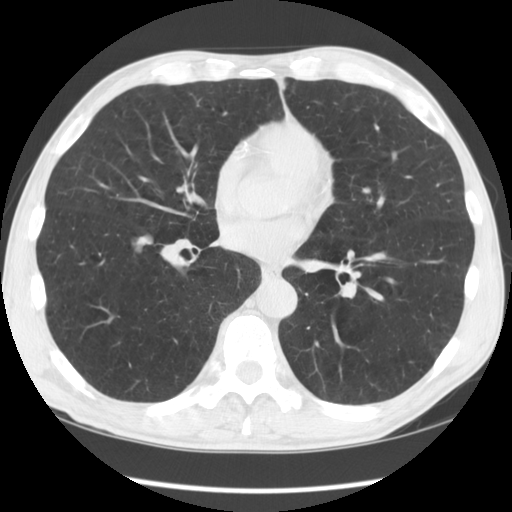
Chest CT (low-dose screening protocol), one axial image; second annual screen; lung window (W 1500 / L -600 HU); 2.5 mm slice thickness; standard (soft-tissue) reconstruction kernel (STANDARD); slice 83 of 135 in the series. Male, age 60 years at enrolment.
Expert reader's lesion annotation, bounding box <111,229,164,269> (left, top, right, bottom; pixels). The exam's reader record, not a measurement of the box and not confirmed to be the same lesion: non-calcified nodule or mass ≥4 mm, right lower lobe, 17 × 14 mm, smooth margins, soft tissue attenuation, pre-existing on the prior screen: yes; interval growth: yes. Lung cancer was diagnosed 39 days after this screen: large cell carcinoma, NOS, right lower lobe, undifferentiated (G4), stage IA (AJCC 6th edition), 16 mm at pathology.